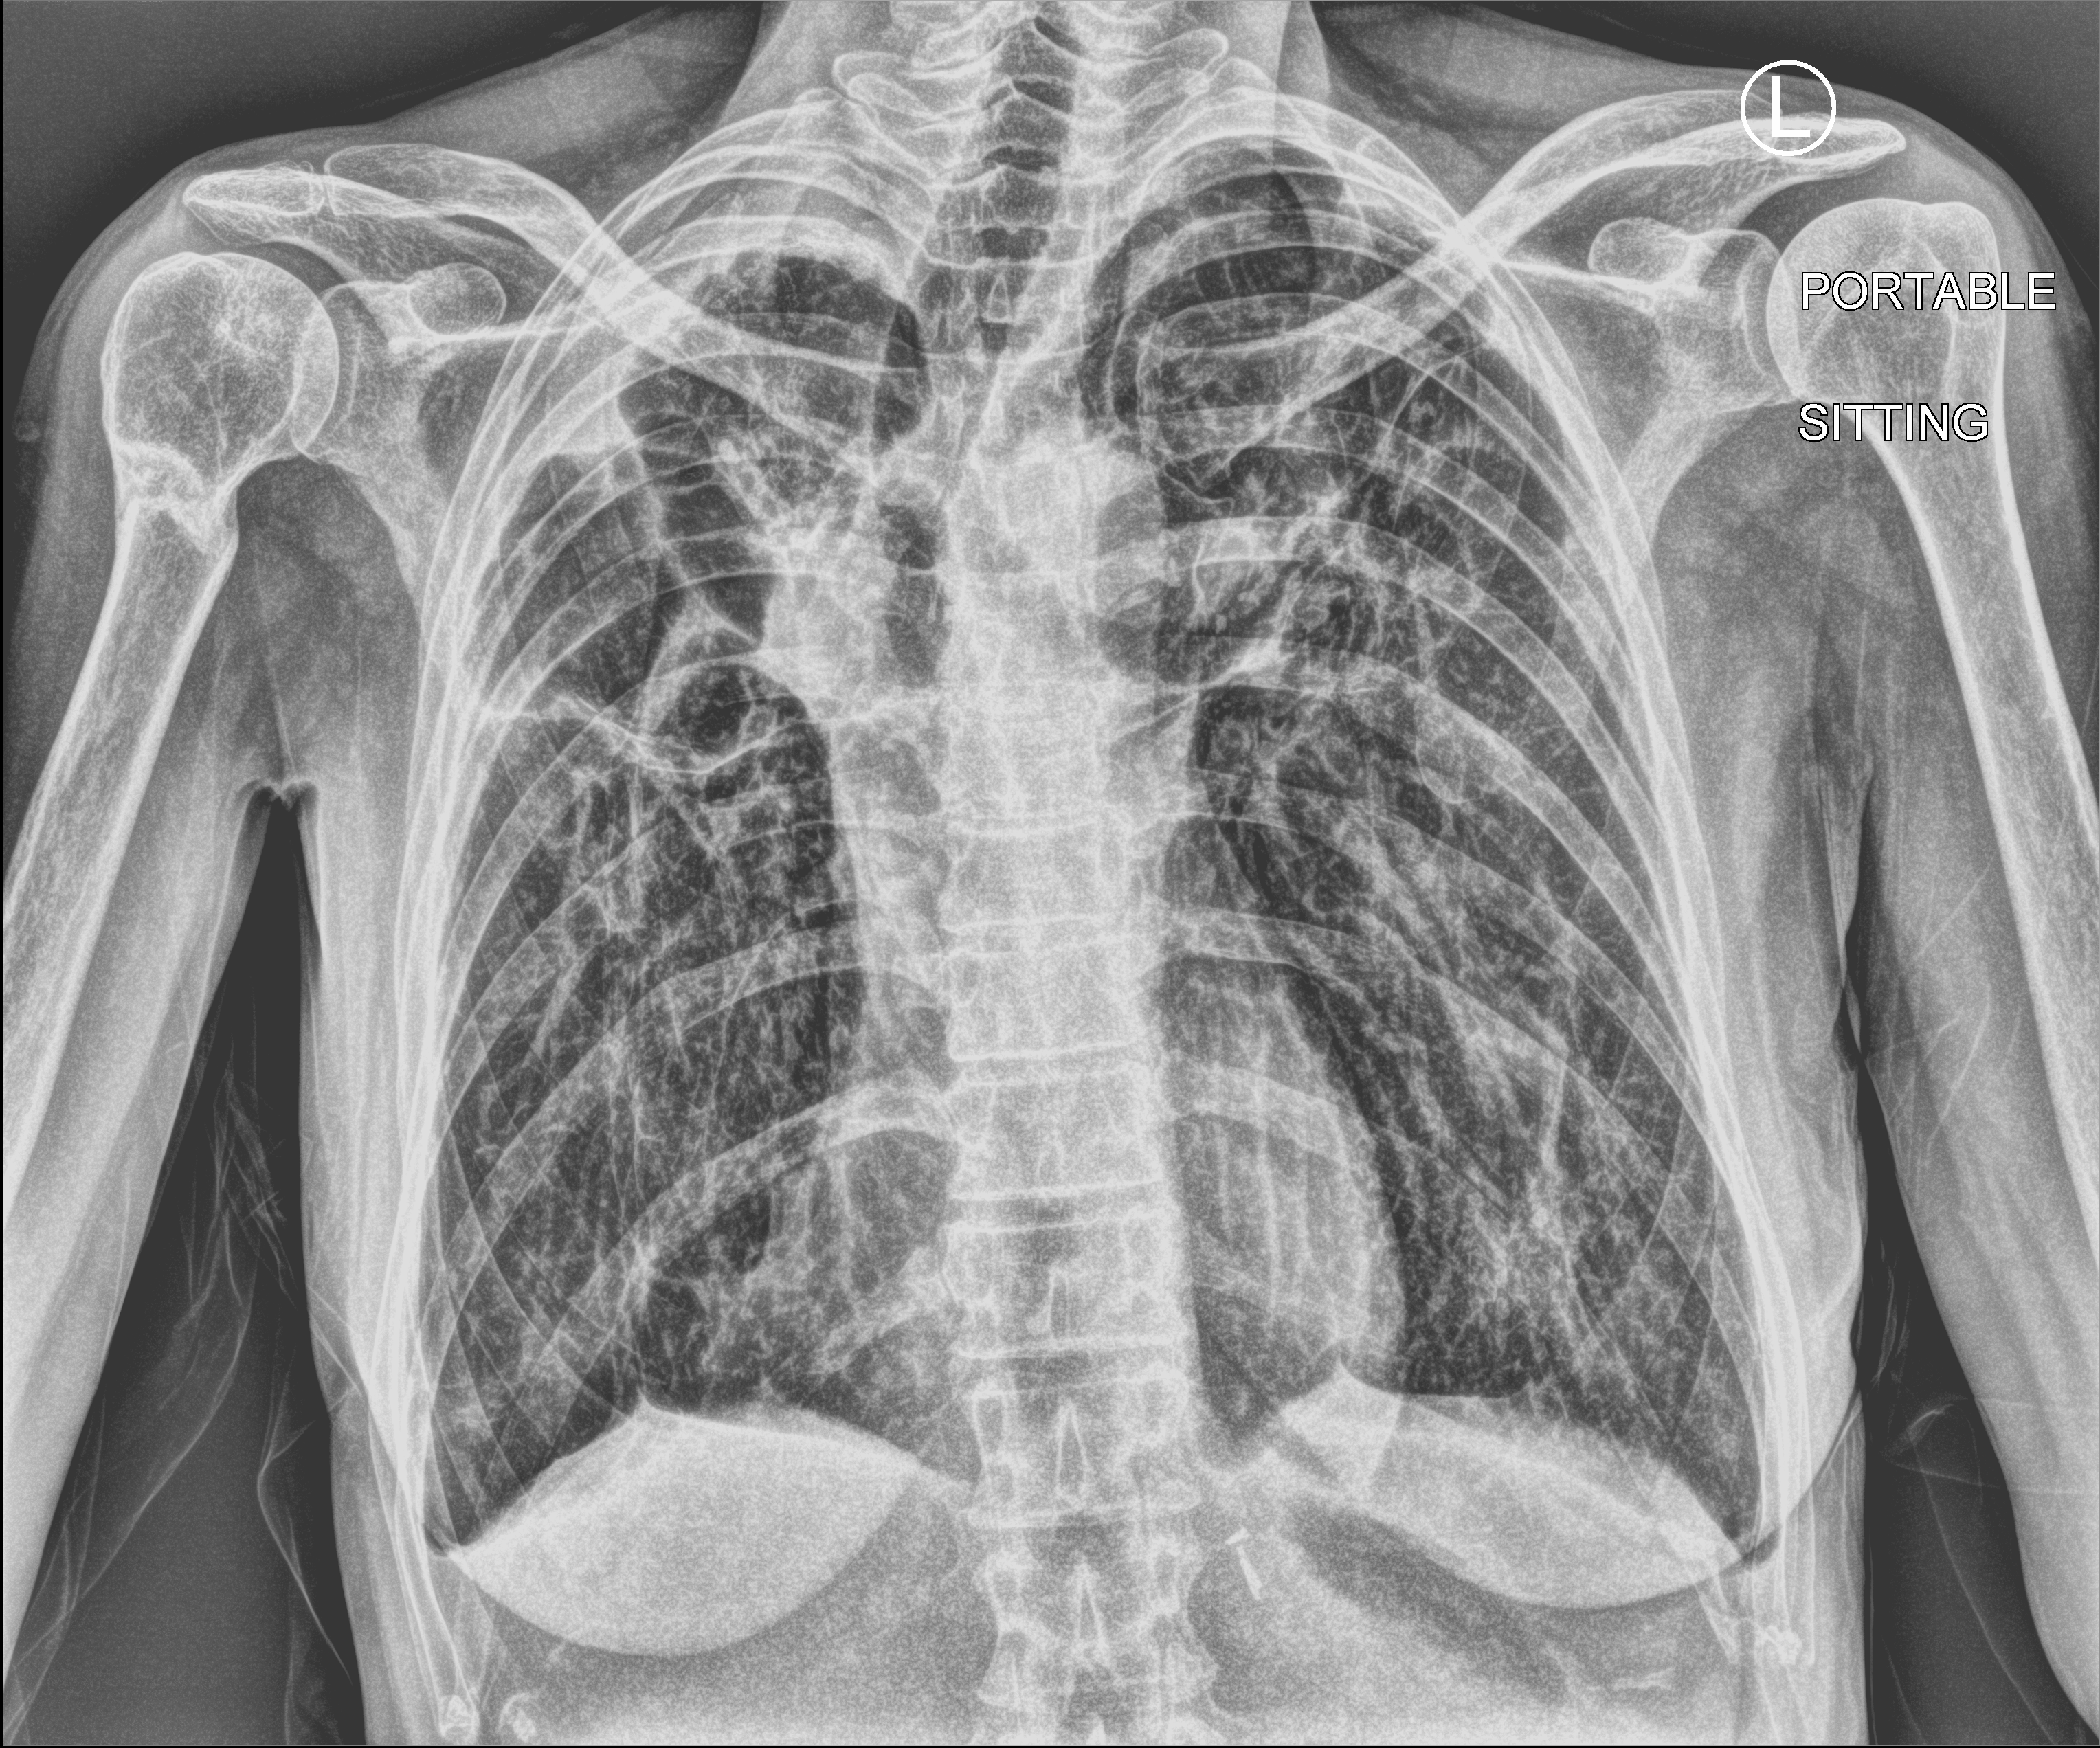
Portable chest radiograph. Female patient hospitalised with COVID-19, age 18–59 years.
Hospital-stay facts (about this admission, not read from this image; timing relative to this image not recorded):
- mechanically ventilated during this hospital stay: no